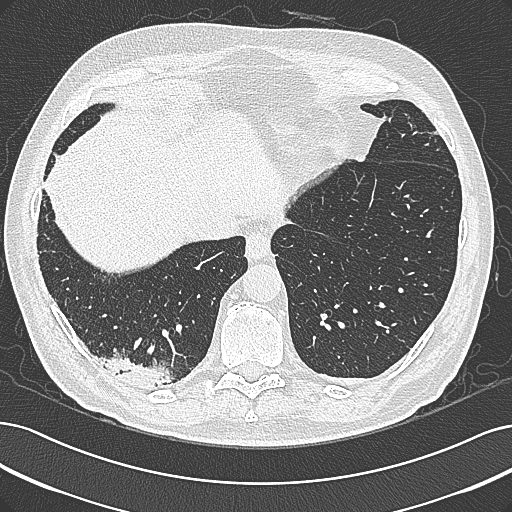
Low-dose screening chest CT, axial slice. Baseline annual screen. Lung window (W 1500 / L -600 HU). 1 mm slice thickness. Lung (sharp) reconstruction kernel (B80f). 120 kVp. 512 × 512 image matrix. Male participant, aged 68 years at enrolment. Former smoker at enrolment.
Expert reader's lesion annotation, box from (x=97, y=341) to (x=184, y=402) px. Screening reader's record for this exam: no non-calcified nodule ≥4 mm recorded. Lung cancer was diagnosed 154 days after this screen: mucinous adenocarcinoma, right lower lobe, well differentiated (G1), stage IB (AJCC 6th edition), 50 mm at pathology.